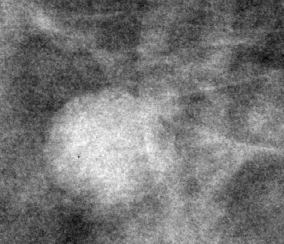
Region of interest cut from a scanned film mammogram (one marked finding); right breast; MLO view; BI-RADS breast density category 2 (scale 1–4).
- Finding: mass, shape round, margins circumscribed; BI-RADS assessment category 2; subtlety rating 5 on a 1 (subtle) to 5 (obvious) scale; benign; no additional work-up was recommended (benign without callback).